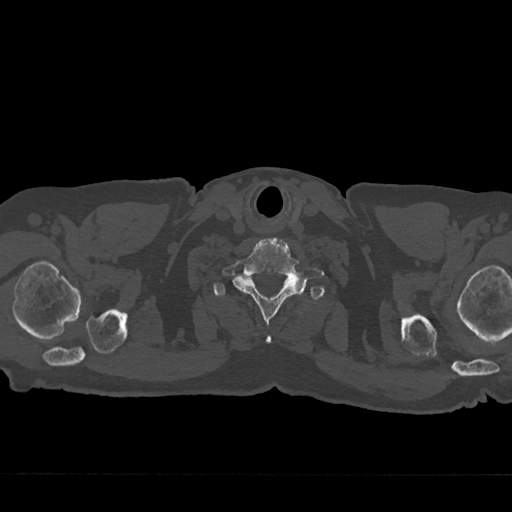
CT including the spine, one axial slice; slice 687 of 797 in the series (ordered by position); reconstruction kernel Br40s/3; bone window (W 1800 / L 400 HU); 0.5 mm slice thickness; 512 × 512 image matrix. Patient: male, 75 years. From the clinical record (not read from this slice): primary cancer: renal; vertebrae with lytic lesions (as recorded): T4.
Annotated regions visible in this slice (semi-automatic segmentation, software-assisted and operator-edited):
- T1 vertebra: box from (x=214, y=279) to (x=303, y=297) px